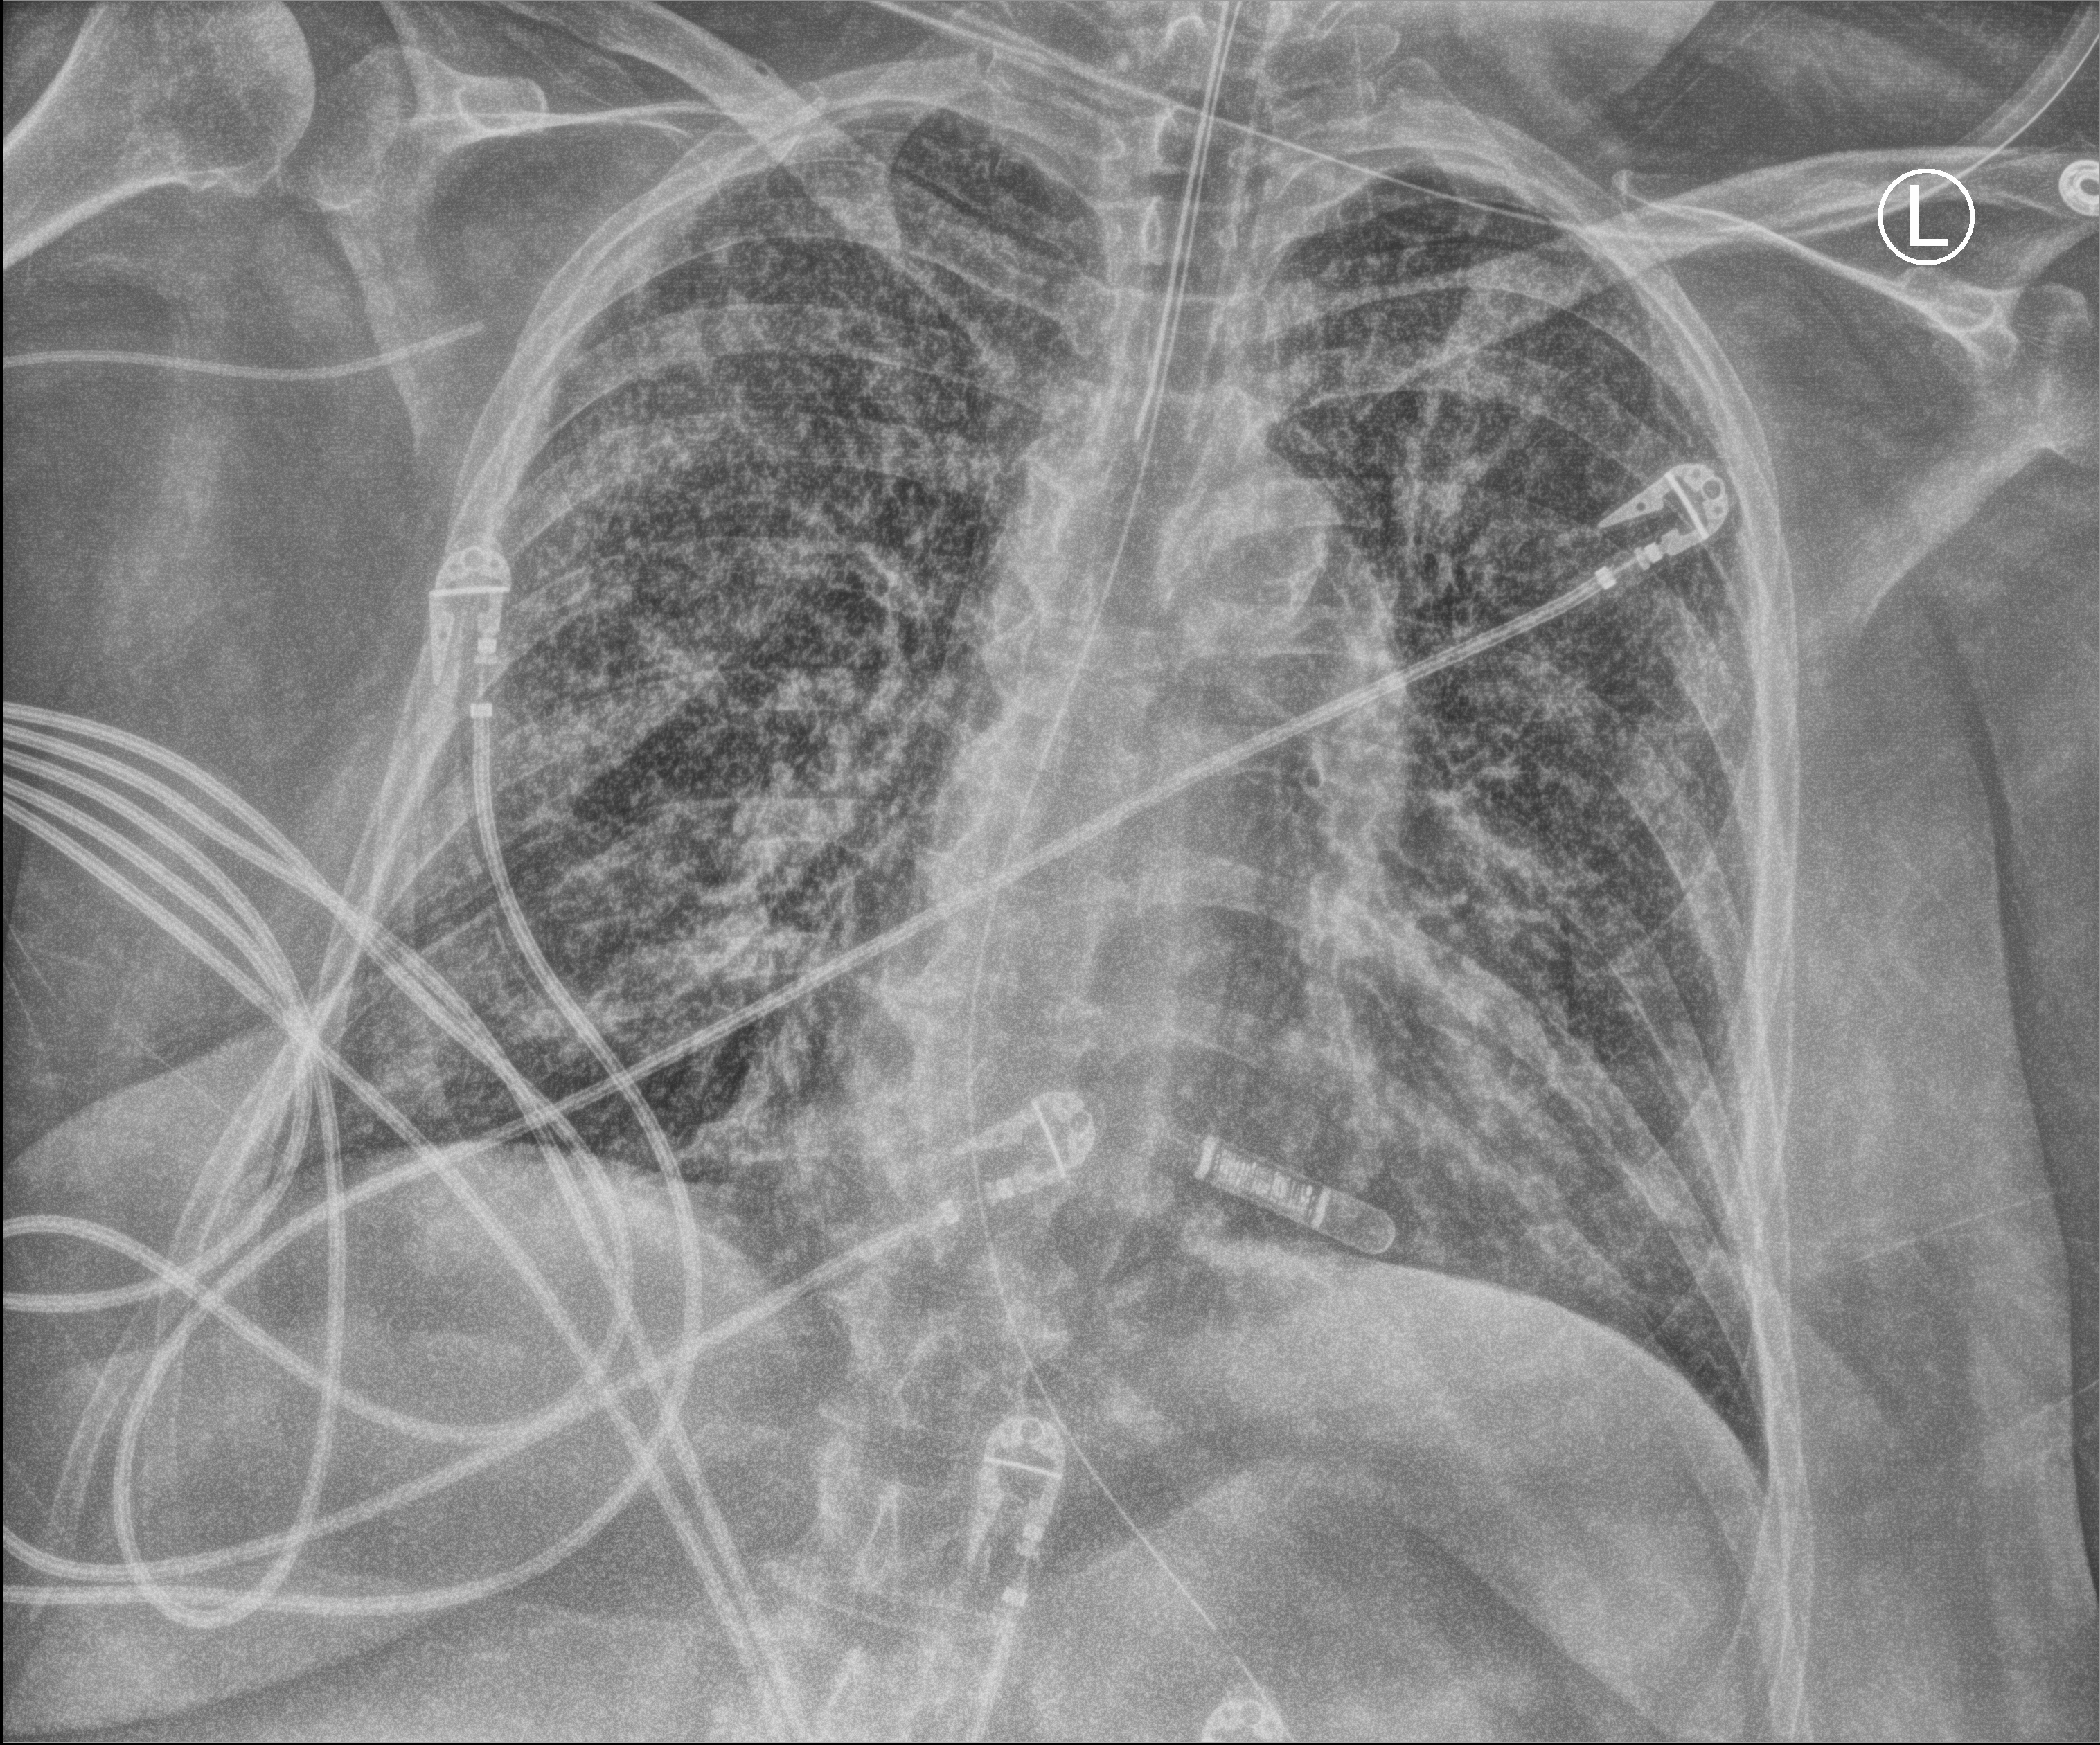
Portable chest radiograph; anteroposterior (AP) projection. Patient hospitalised with COVID-19; female, aged 60–74 years.
From the hospital-stay record, not from the radiograph (when in the stay this image was taken is not recorded):
- length of hospital stay: 28 days